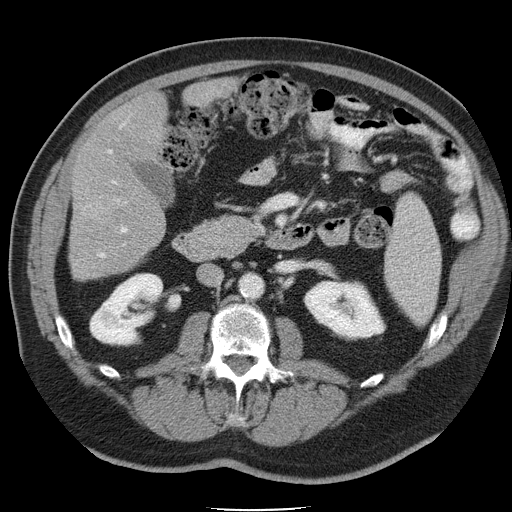
Contrast-enhanced abdominal CT, one axial slice. Slice 16 of 45 in the series (ordered by position). 120 kVp. Intravenous contrast given. Soft-tissue window (W 400 / L 40 HU). 5 mm slice thickness. 512 × 512 image matrix. Male patient, age 65 years. Case-level facts recorded for this patient, not image findings: diagnosis: colorectal cancer liver metastases, imaged before liver resection; multiple liver metastases: yes; largest metastasis: 4.9 cm; disease in both lobes: no.
Outlined on this slice (manually delineated by an expert):
- hepatic veins: box from (x=98, y=150) to (x=111, y=258) px
- liver: (x=70, y=82)–(x=228, y=280)
- planned liver remnant (the part of the liver to remain after resection): (x=92, y=82)–(x=227, y=168)
- portal vein (with intrahepatic branches): (x=113, y=181)–(x=127, y=232)